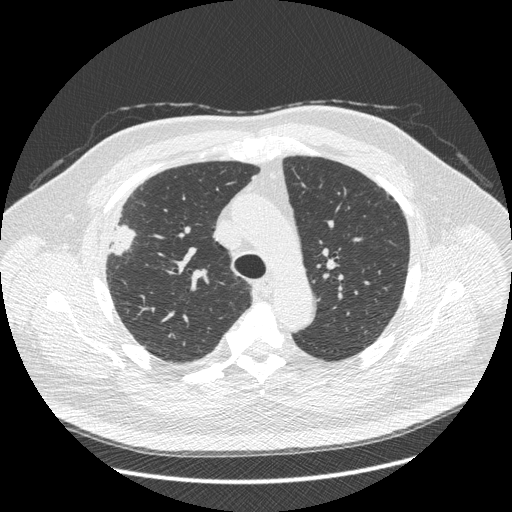
Low-dose screening chest CT, one axial slice. Position 306 of 426 along the scan axis. 120 kVp. Lung window (W 1500 / L -600 HU). 1.25 mm slice thickness. 512 × 512 image matrix, field of view 400 × 400 mm.
Outlined on this slice (expert manual segmentation):
- lesion 1 (tumor, upper lobe of right lung): bounding box (x1, y1, x2, y2) in pixels: (110, 225, 135, 255)